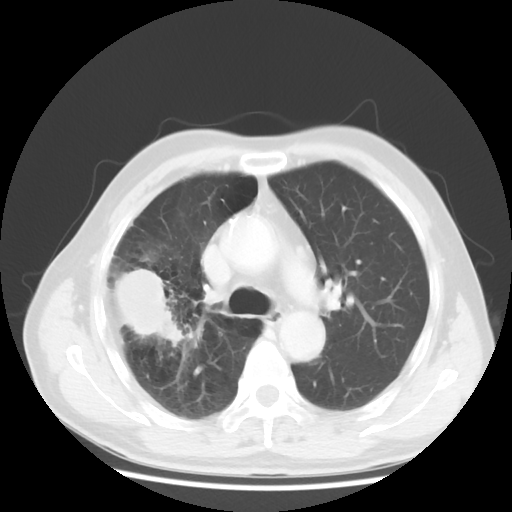
Chest CT, one axial slice. Slice 32 of 50 in the series (ordered by position). Reconstruction kernel STANDARD. 120 kVp. Lung window (W 1500 / L -600 HU). 5 mm slice thickness. 512 × 512 image matrix, field of view 360 × 360 mm. Patient: male, 69 years. Case-level facts recorded for this patient, not image findings: clinical TNM (as recorded): T3 N0 M0.
Annotated regions visible in this slice (rectangle marked by the reading radiologist):
- lung tumour (recorded histology: adenocarcinoma): bounding box <112,268,186,350> (left, top, right, bottom; pixels)